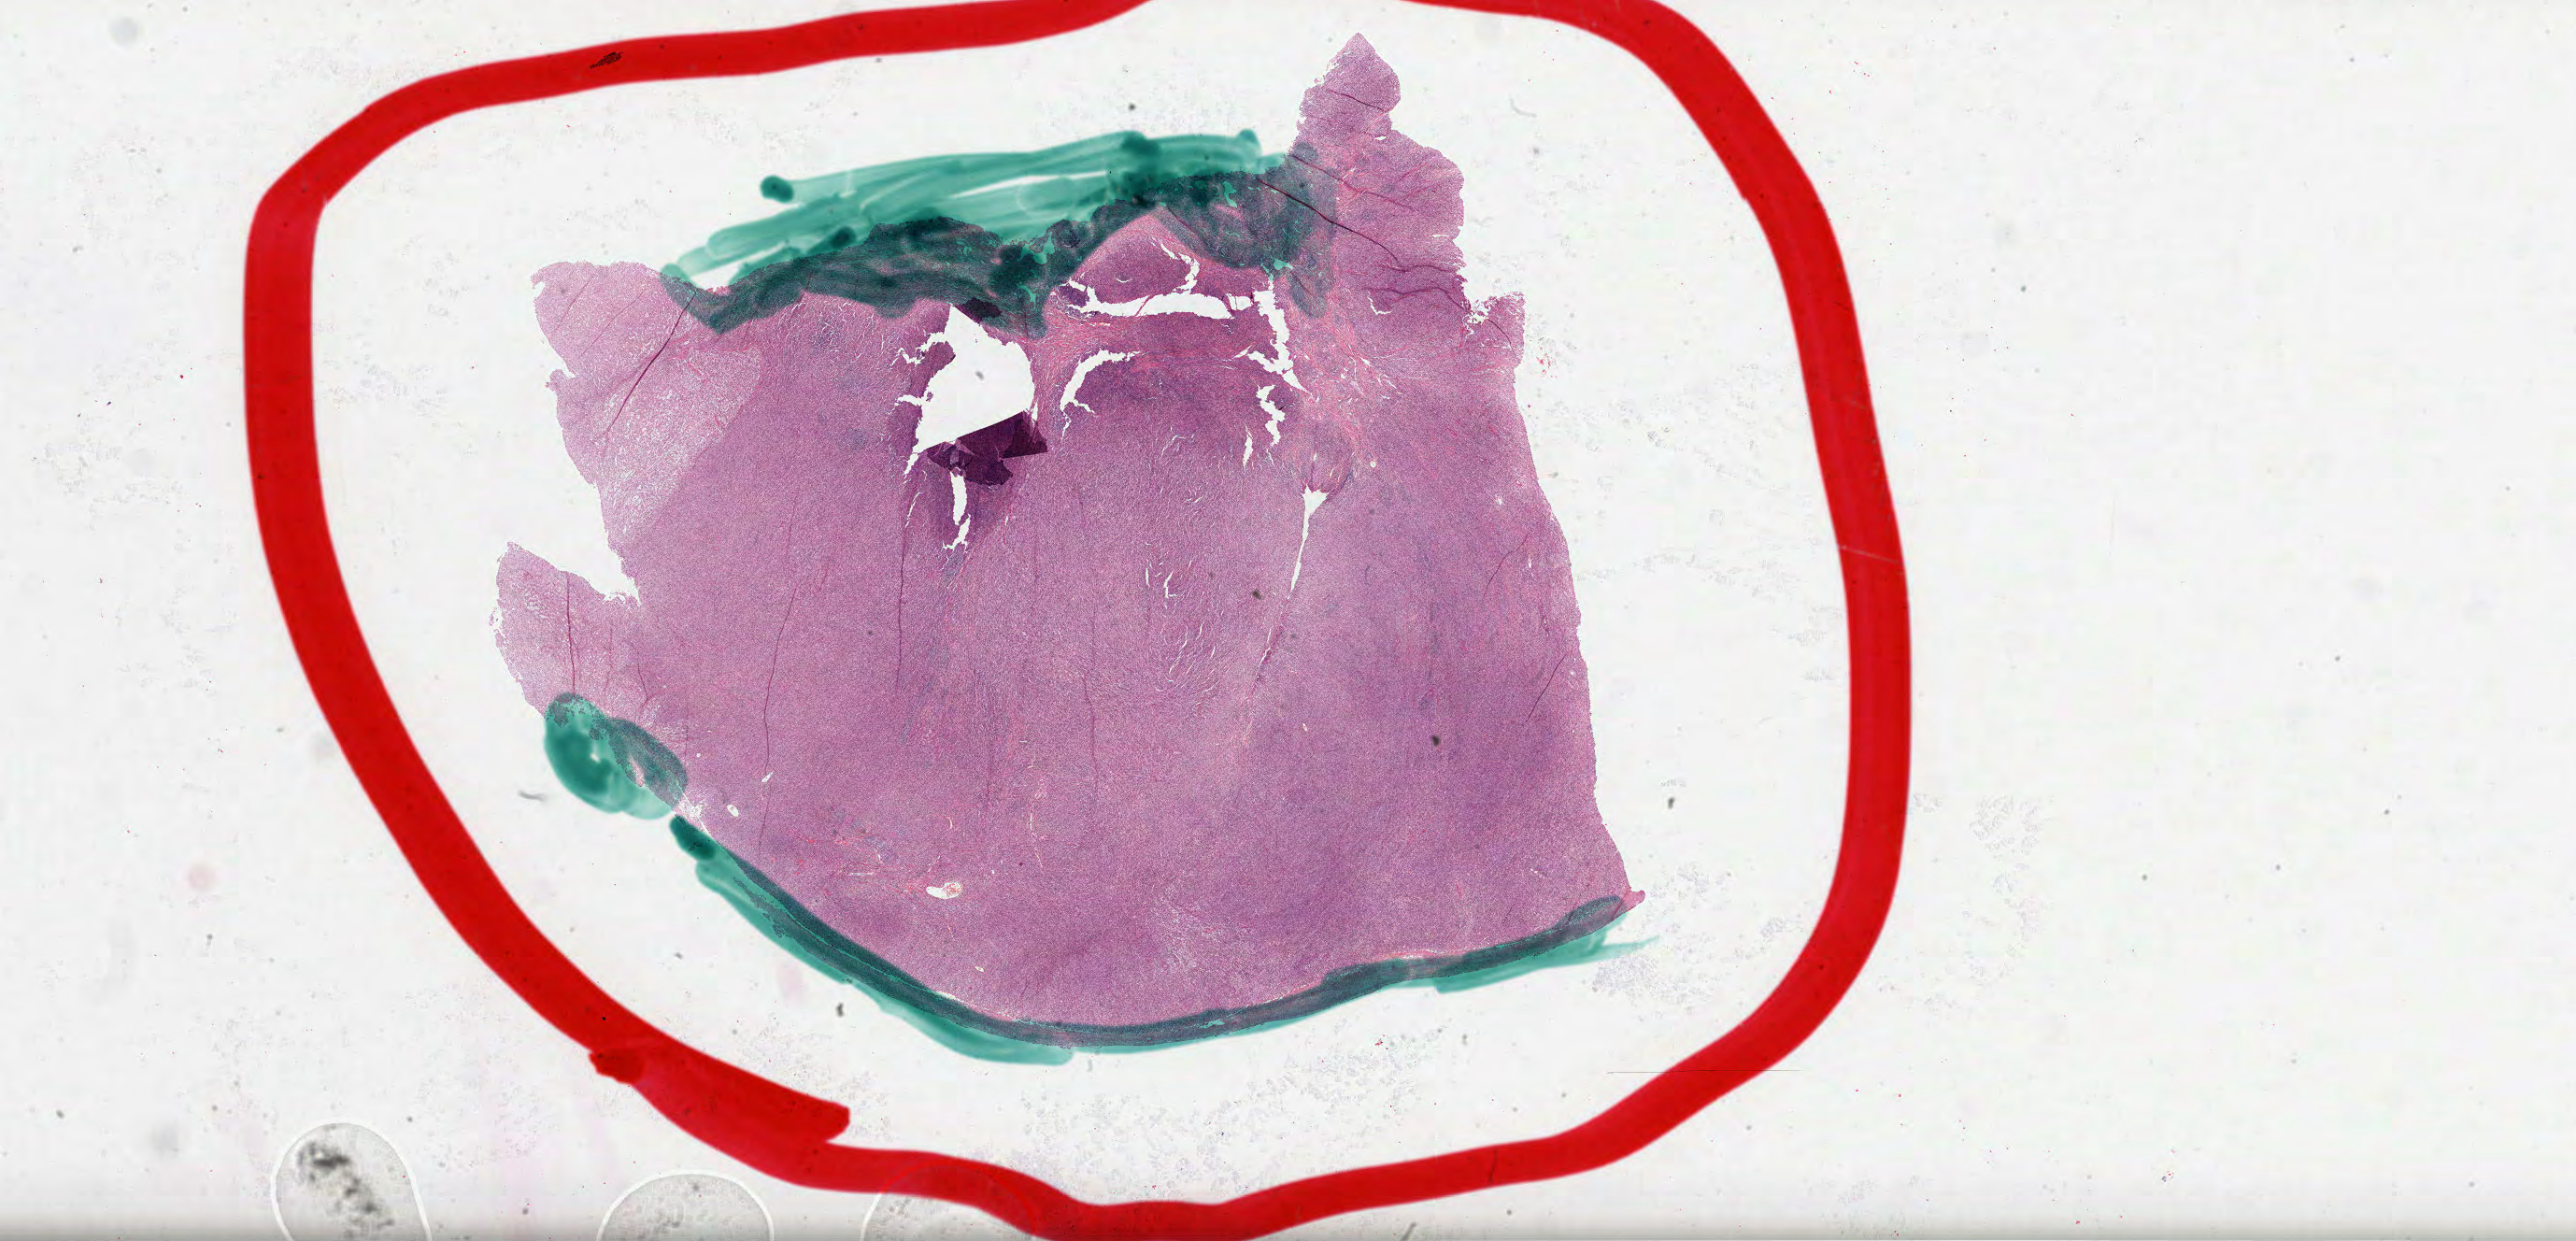
Whole-slide histology image, H&E, shown as a low-resolution overview of the whole scanned area (about 44.5 x 21.4 mm, slide scanned at 40x). Formalin-fixed paraffin-embedded (FFPE) diagnostic section. Primary tumour sample from the stomach. Patient: female, age at initial diagnosis 57 years. Histologic grade: G3 (poorly differentiated).
* TNM: T3 N3a M0
* histologic diagnosis: Adenocarcinoma, NOS
* lymph nodes positive (case pathology): 15 of 15 examined
* AJCC pathologic stage: IIIB (7th edition)